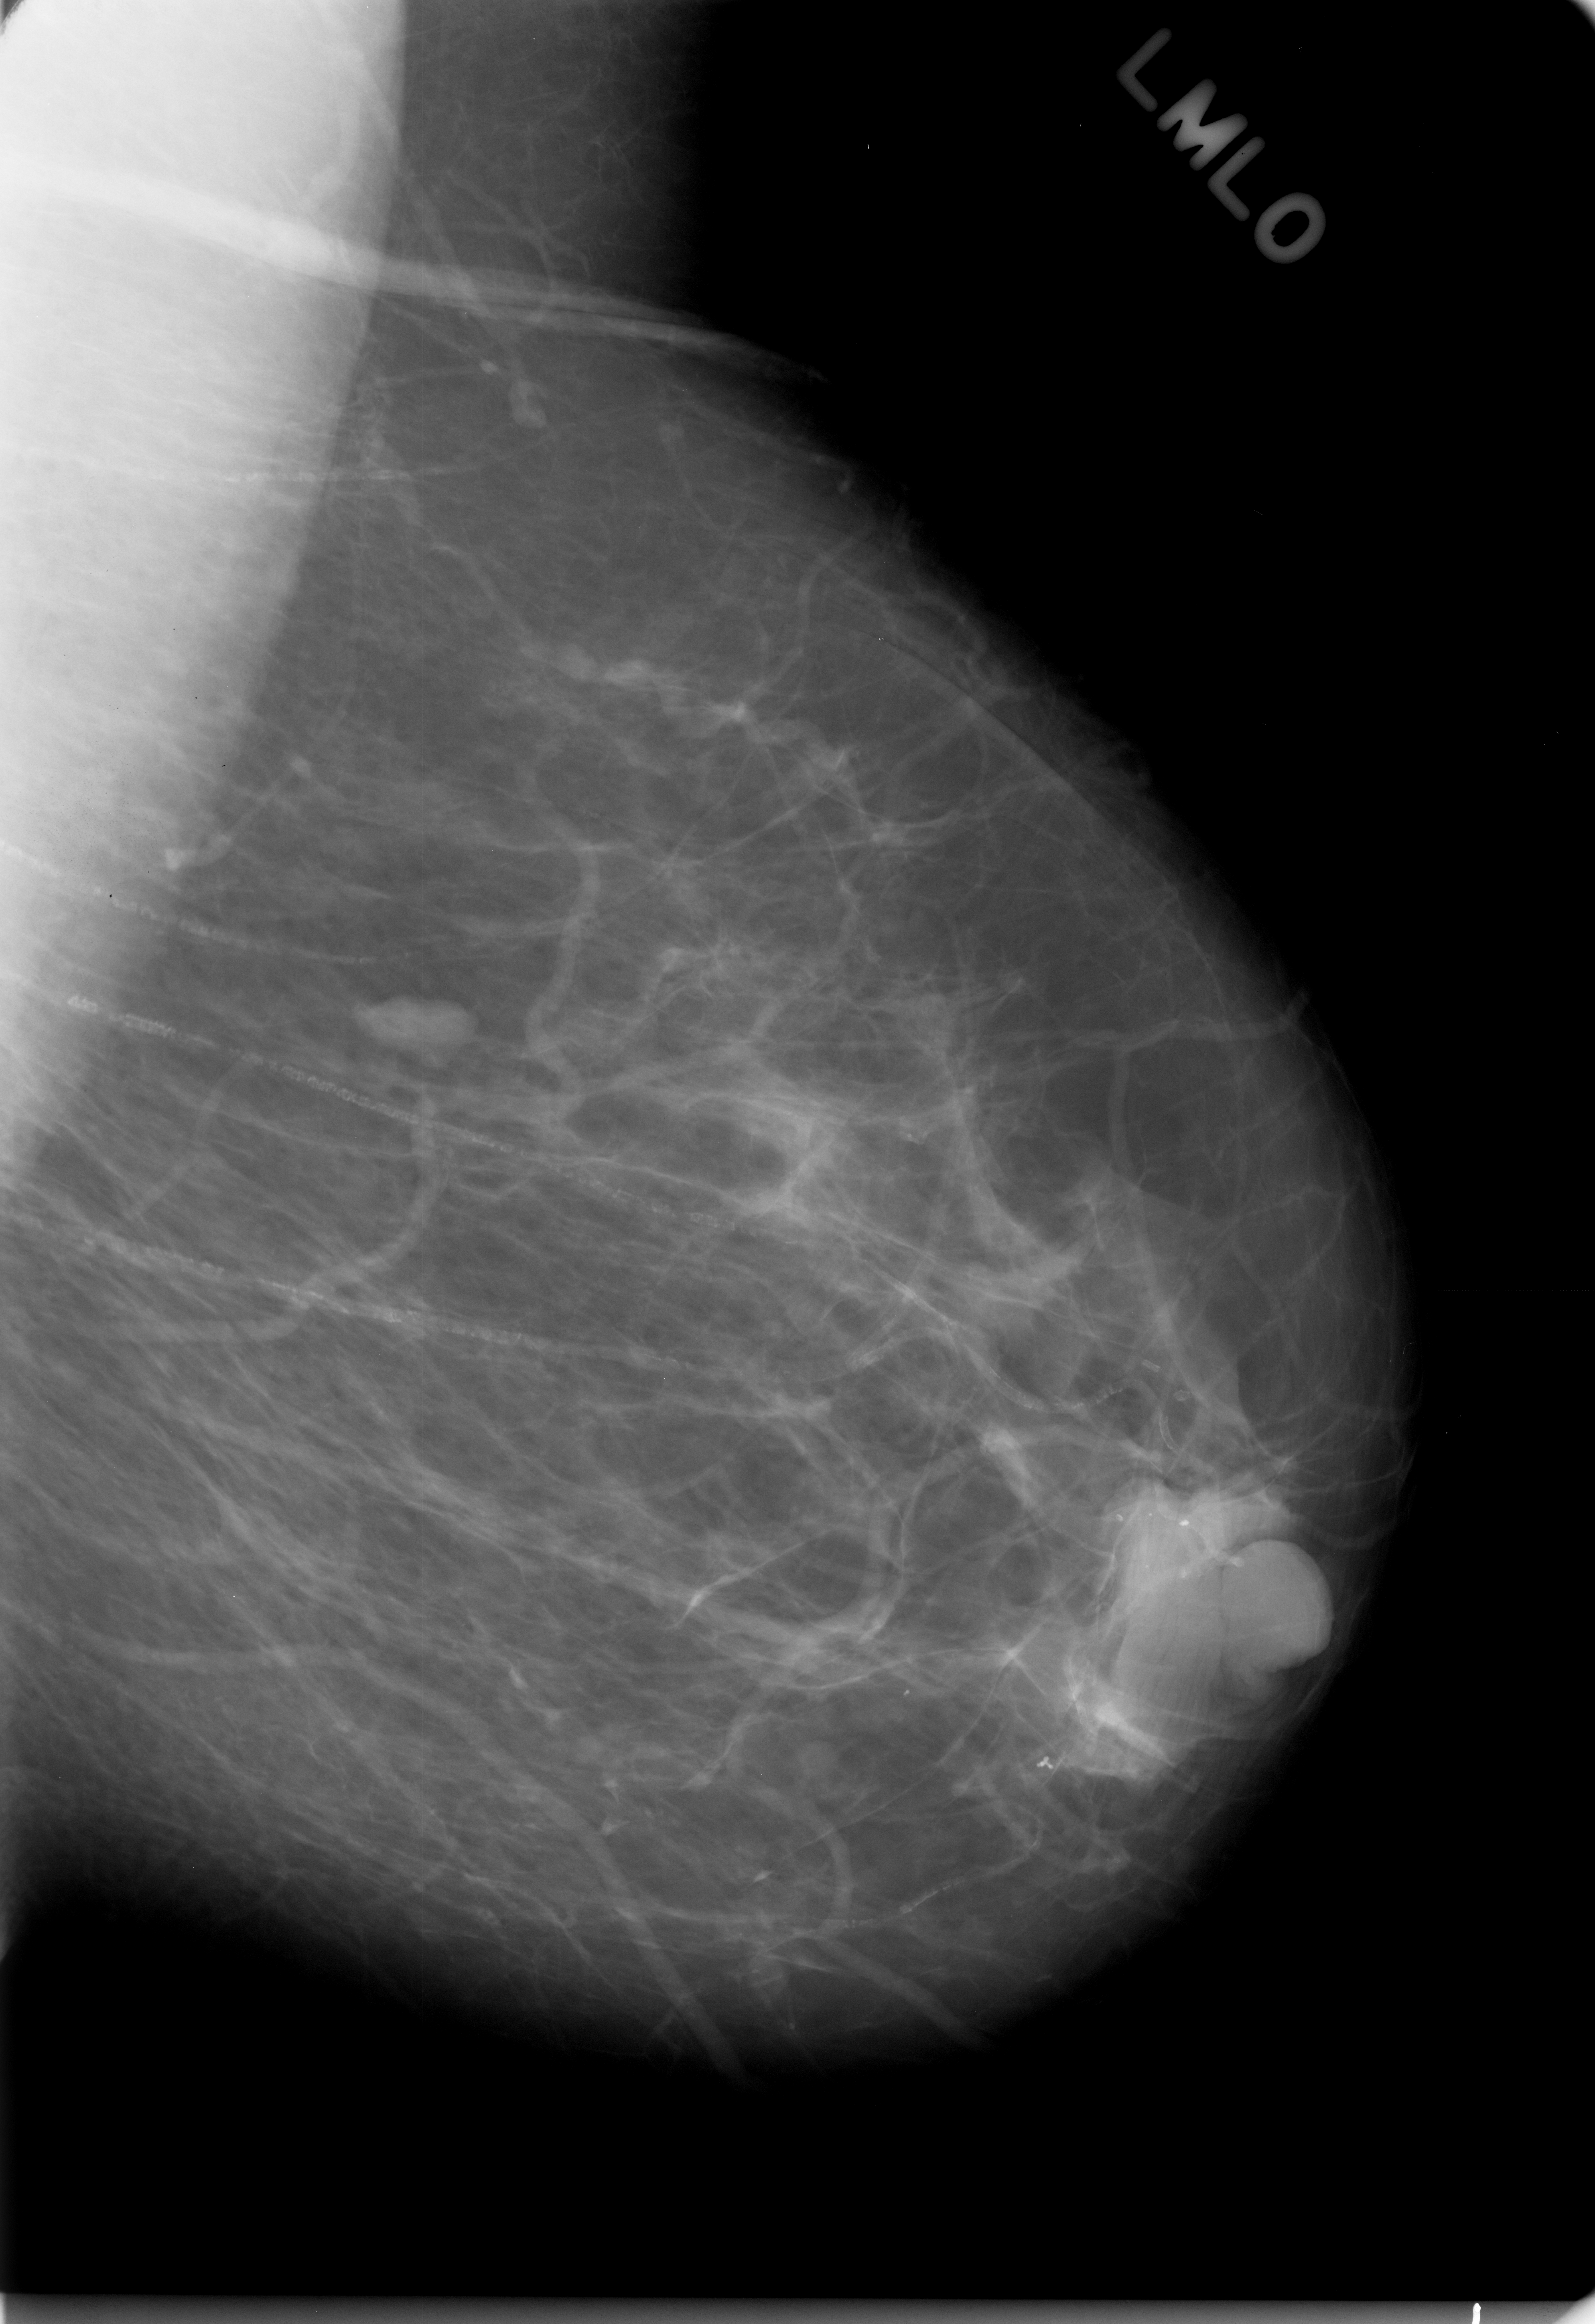
Mammogram (digitized film); left breast; mediolateral oblique (MLO) view; 1595 × 2324 image matrix.
Marked abnormalities (boxes around the expert regions of interest):
- mass, shape oval, margins circumscribed; BI-RADS assessment category 2; pathology result (as recorded, not read from the image): benign: bounding box [x1, y1, x2, y2] px = [343, 991, 474, 1079]